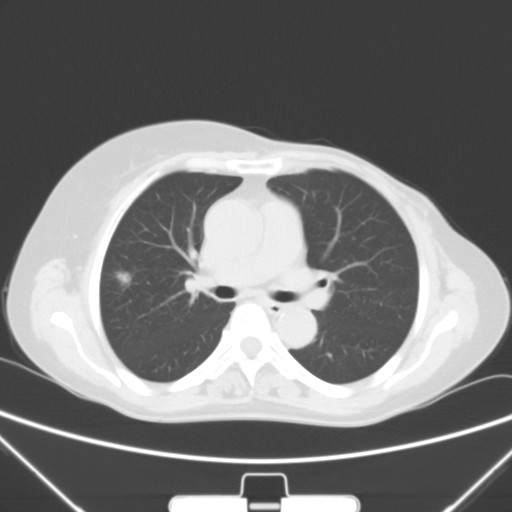
Chest CT, one axial slice. Position 31 of 53 along the scan axis. 120 kVp. Lung window (W 1500 / L -600 HU). 5 mm slice thickness. 512 × 512 image matrix, field of view 350 × 350 mm. Female patient, age 64 years. From the clinical record (not read from this slice): clinical TNM (as recorded): T1c N0 M0; histopathological grade: G1-2.
Structures marked on this image (bounding box drawn by a radiologist):
- lung tumour (recorded histology: adenocarcinoma): bounding box (x1, y1, x2, y2) in pixels: (112, 262, 137, 289)